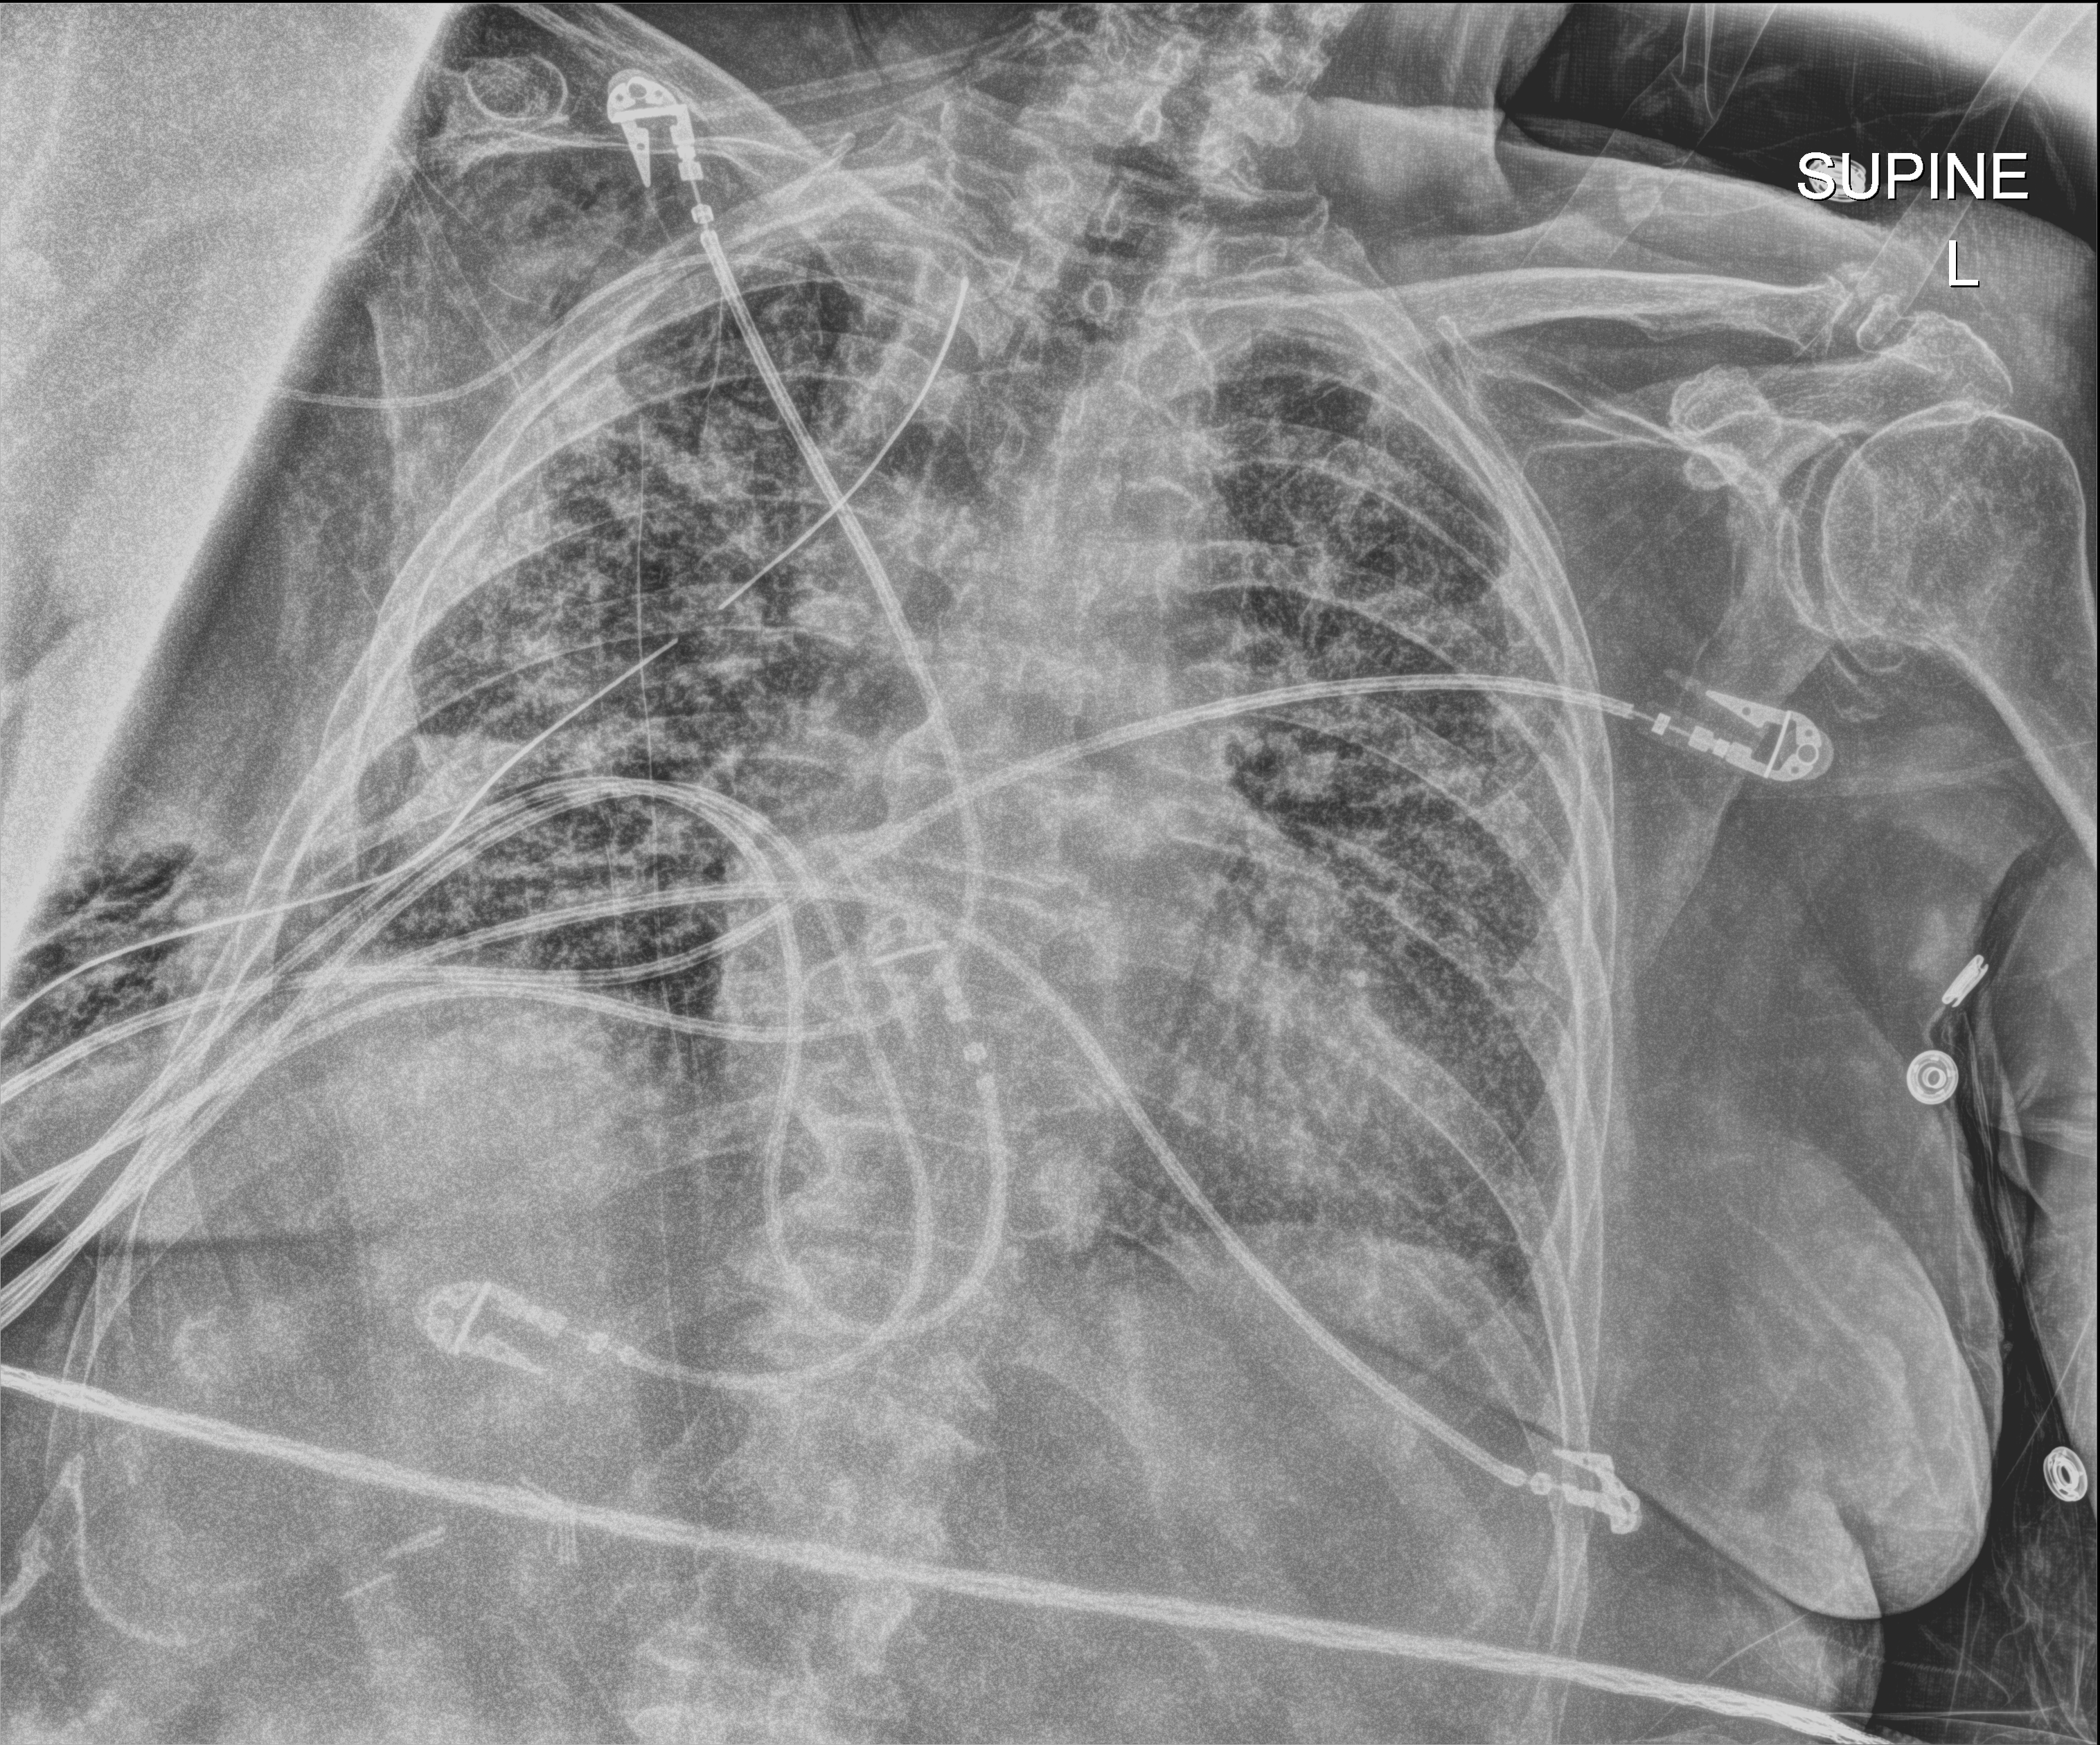
Chest radiograph. Female patient hospitalised with COVID-19, age 75–90 years.
Hospital-stay facts (about this admission, not read from this image; timing relative to this image not recorded):
- admitted to intensive care during this hospital stay: no
- mechanically ventilated during this hospital stay: yes
- smoking status (admission record): former